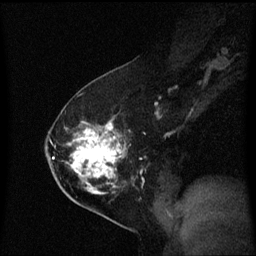
Breast MRI (dynamic contrast-enhanced), one sagittal slice; slice 36 of 60 in the series (ordered by position); dynamic contrast-enhanced series, image 2 of 3 at this slice position (ordered by acquisition); 1.5 T; TE 4.2 ms, TR 8.4 ms; 256 × 256 image matrix. Patient: female, 54 years. Case-level facts recorded for this patient, not image findings: setting: breast cancer imaged before/during neoadjuvant chemotherapy; receptor status: HER2-positive.
Structures marked on this image (semi-automatic segmentation, software-assisted and operator-edited):
- analysis volume of interest (the breast-tissue region the enhancement analysis was run in; not a lesion): bounding box <59,122,140,199> (left, top, right, bottom; pixels)
- tumour enhancement mask (voxels above the 70 % enhancement threshold inside the analysis volume of interest): <70,123,123,195>